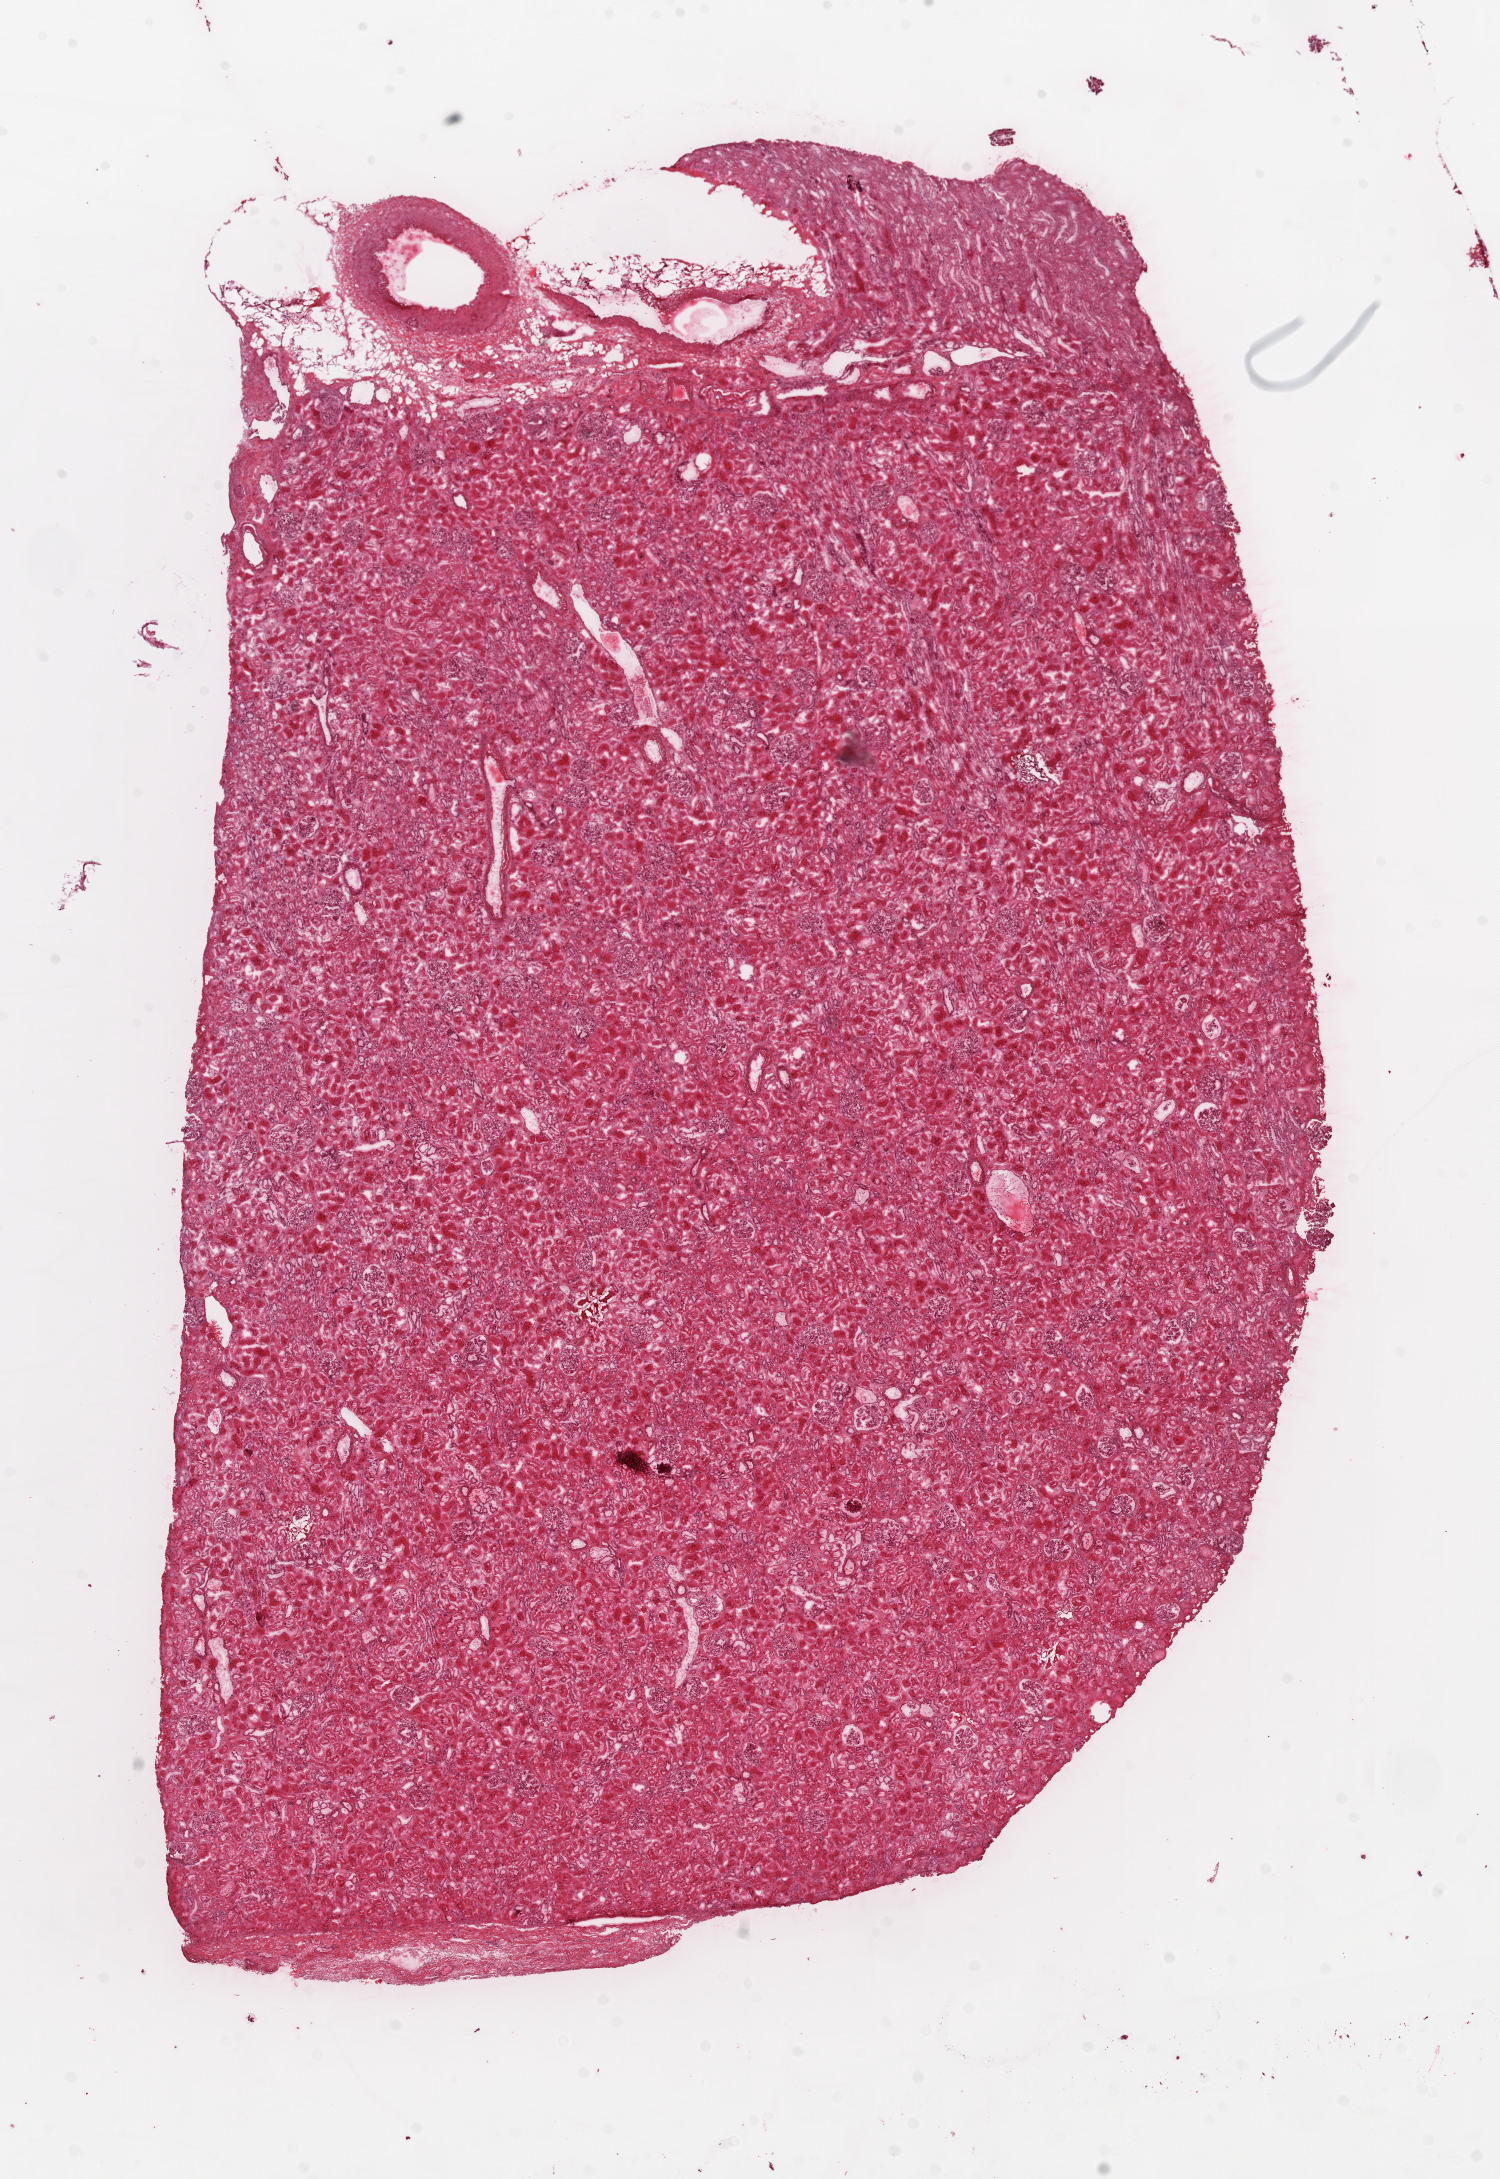
Digitized H&E tissue section (whole slide), whole scanned area (about 12.0 x 17.5 mm, acquisition: 20x scan) shown as a low-resolution overview. Frozen section. Kidney, solid tissue normal (non-tumour tissue) sample. Patient: male, age at initial diagnosis 63 years.
This section: solid tissue normal (non-tumour) sample from the same patient. Patient diagnosis: Clear cell adenocarcinoma, NOS.